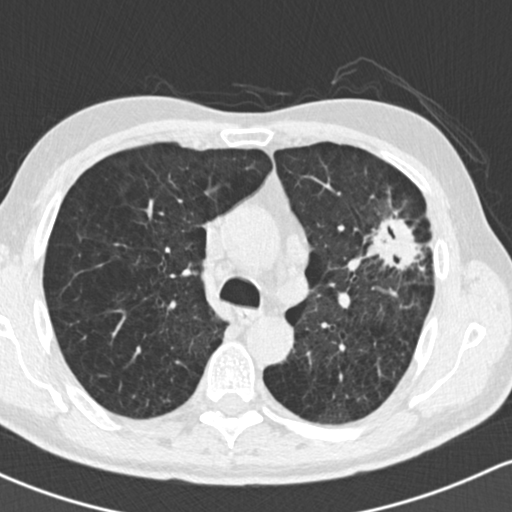
Axial slice from a low-dose chest CT screening exam, baseline annual screen, lung window (W 1500 / L -600 HU), 2 mm slice thickness, slice 58 of 162 in the series. Male, age 61 years at enrolment. Former smoker at enrolment.
- Expert reader's lesion annotation, bounding box (x1, y1, x2, y2) in pixels: (354, 185, 450, 291).
- The exam's reader record, not a measurement of the box and not confirmed to be the same lesion: non-calcified nodule or mass ≥4 mm, left upper lobe, 35 × 35 mm, spiculated (stellate) margins, soft tissue attenuation.
- Participant outcome: lung cancer diagnosed 19 days after this screen — adenocarcinoma, NOS, left upper lobe, well differentiated (G1), stage IIIA (AJCC 6th edition), 45 mm at pathology.